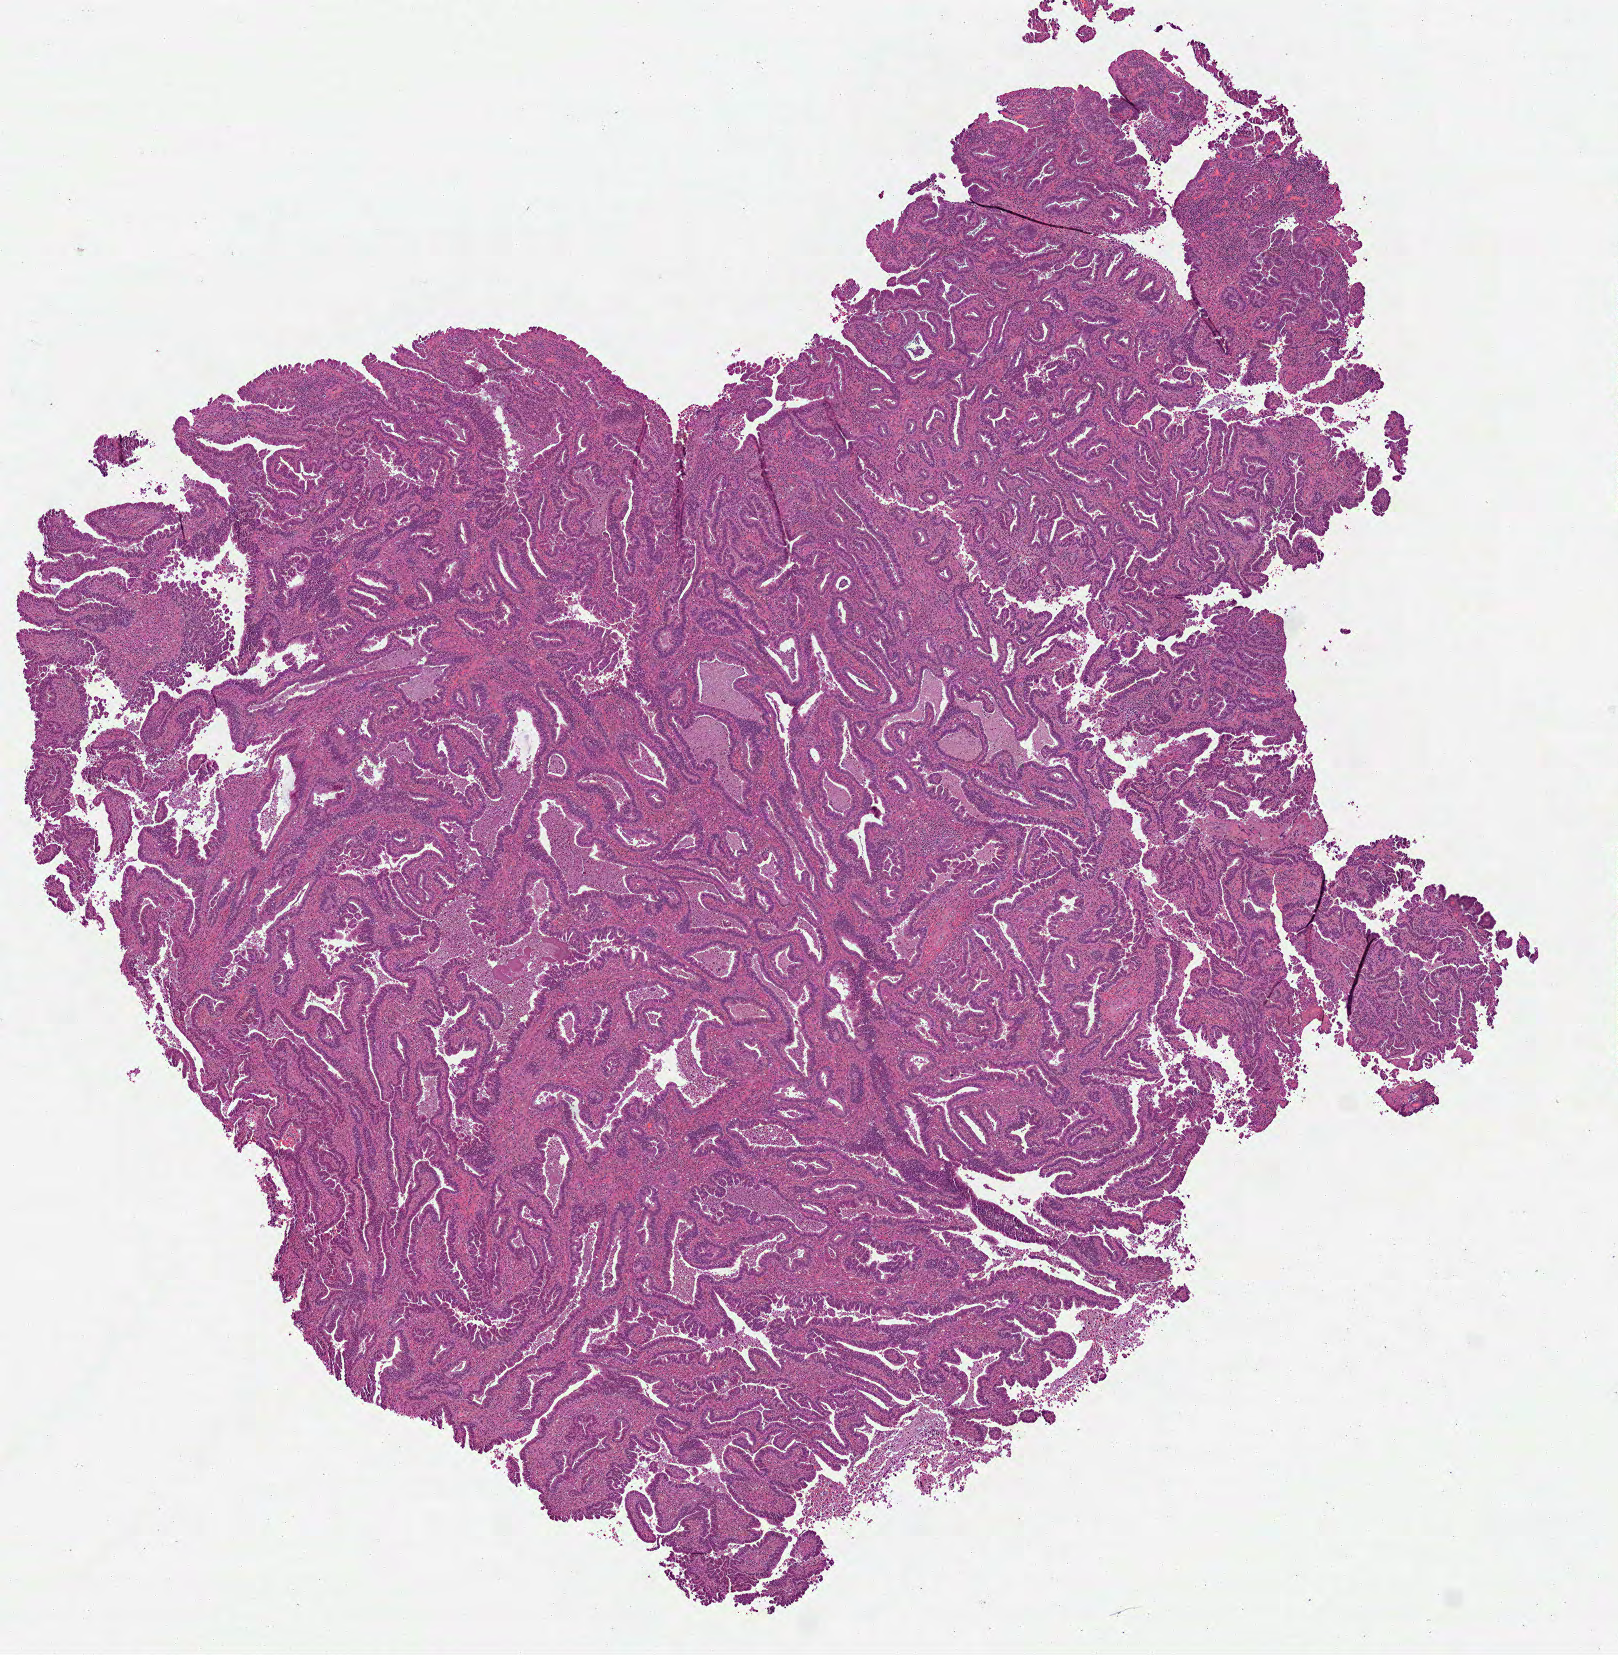
Whole-slide histology image, H&E-stained, low-resolution overview of the scanned area, about 6.5 x 6.7 mm (slide scanned at 40x). Formalin-fixed paraffin-embedded (FFPE) diagnostic section. Sample: primary tumour, cervix. Patient: female, age at initial diagnosis 38 years. Histologic grade: G3 (poorly differentiated).
Histologic diagnosis: Adenocarcinoma, endocervical type (cervix uteri). Lymph nodes positive (case pathology): 4 of 28 examined. FIGO stage: IIIB.